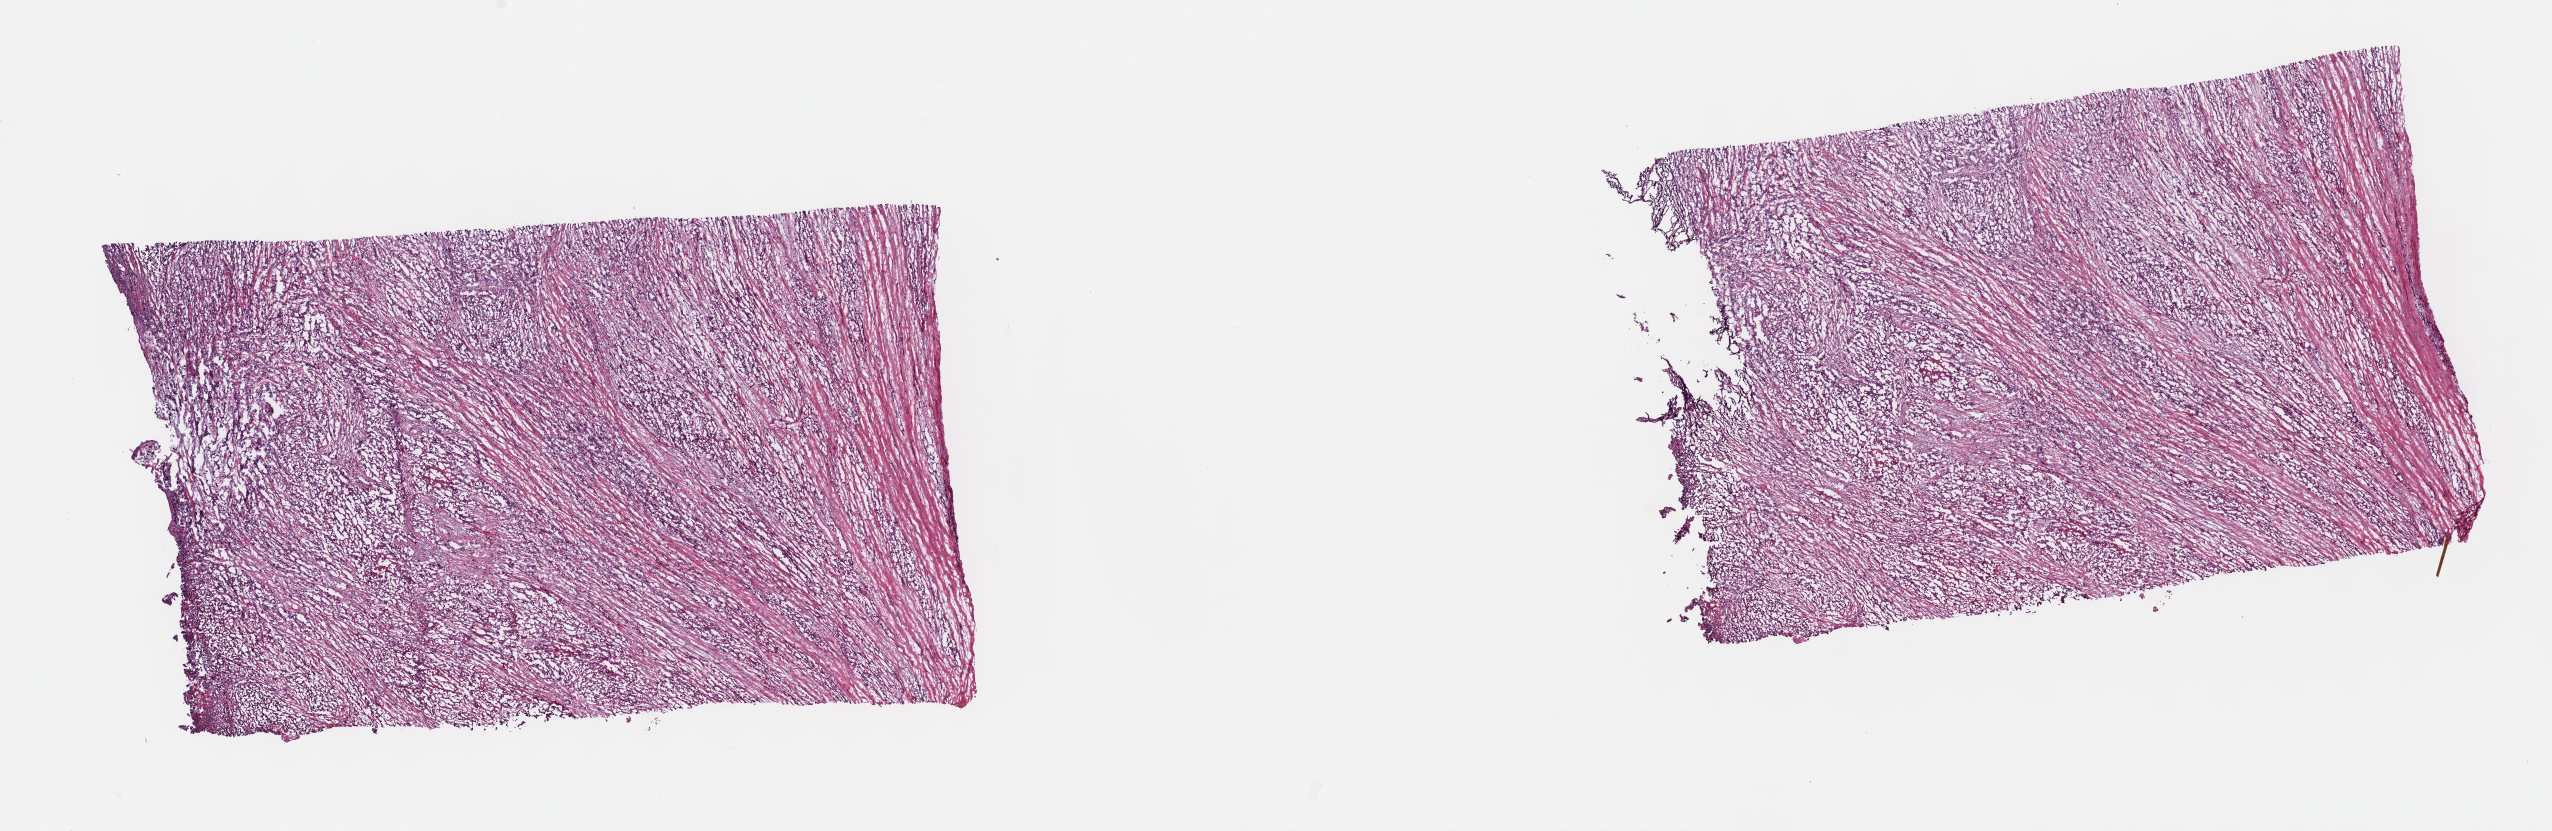
H&E-stained whole-slide image, a low-resolution overview of the entire scanned area, about 20.6 x 6.7 mm (acquisition: 40x scan), frozen section, sample: primary tumour, mesothelium. Male patient; age at initial diagnosis 52 years. Pathologist review of this section (percent, as recorded): tumour cells 100%, tumour nuclei 70%, normal cells 0%, stromal cells 0%, necrosis 0%. Infiltration values recorded for this section: lymphocyte infiltration 1%, monocyte infiltration 0%, neutrophil infiltration 0%.
Pathologic diagnosis: Epithelioid mesothelioma, malignant (pleura, NOS). AJCC pathologic stage: I (6th edition).